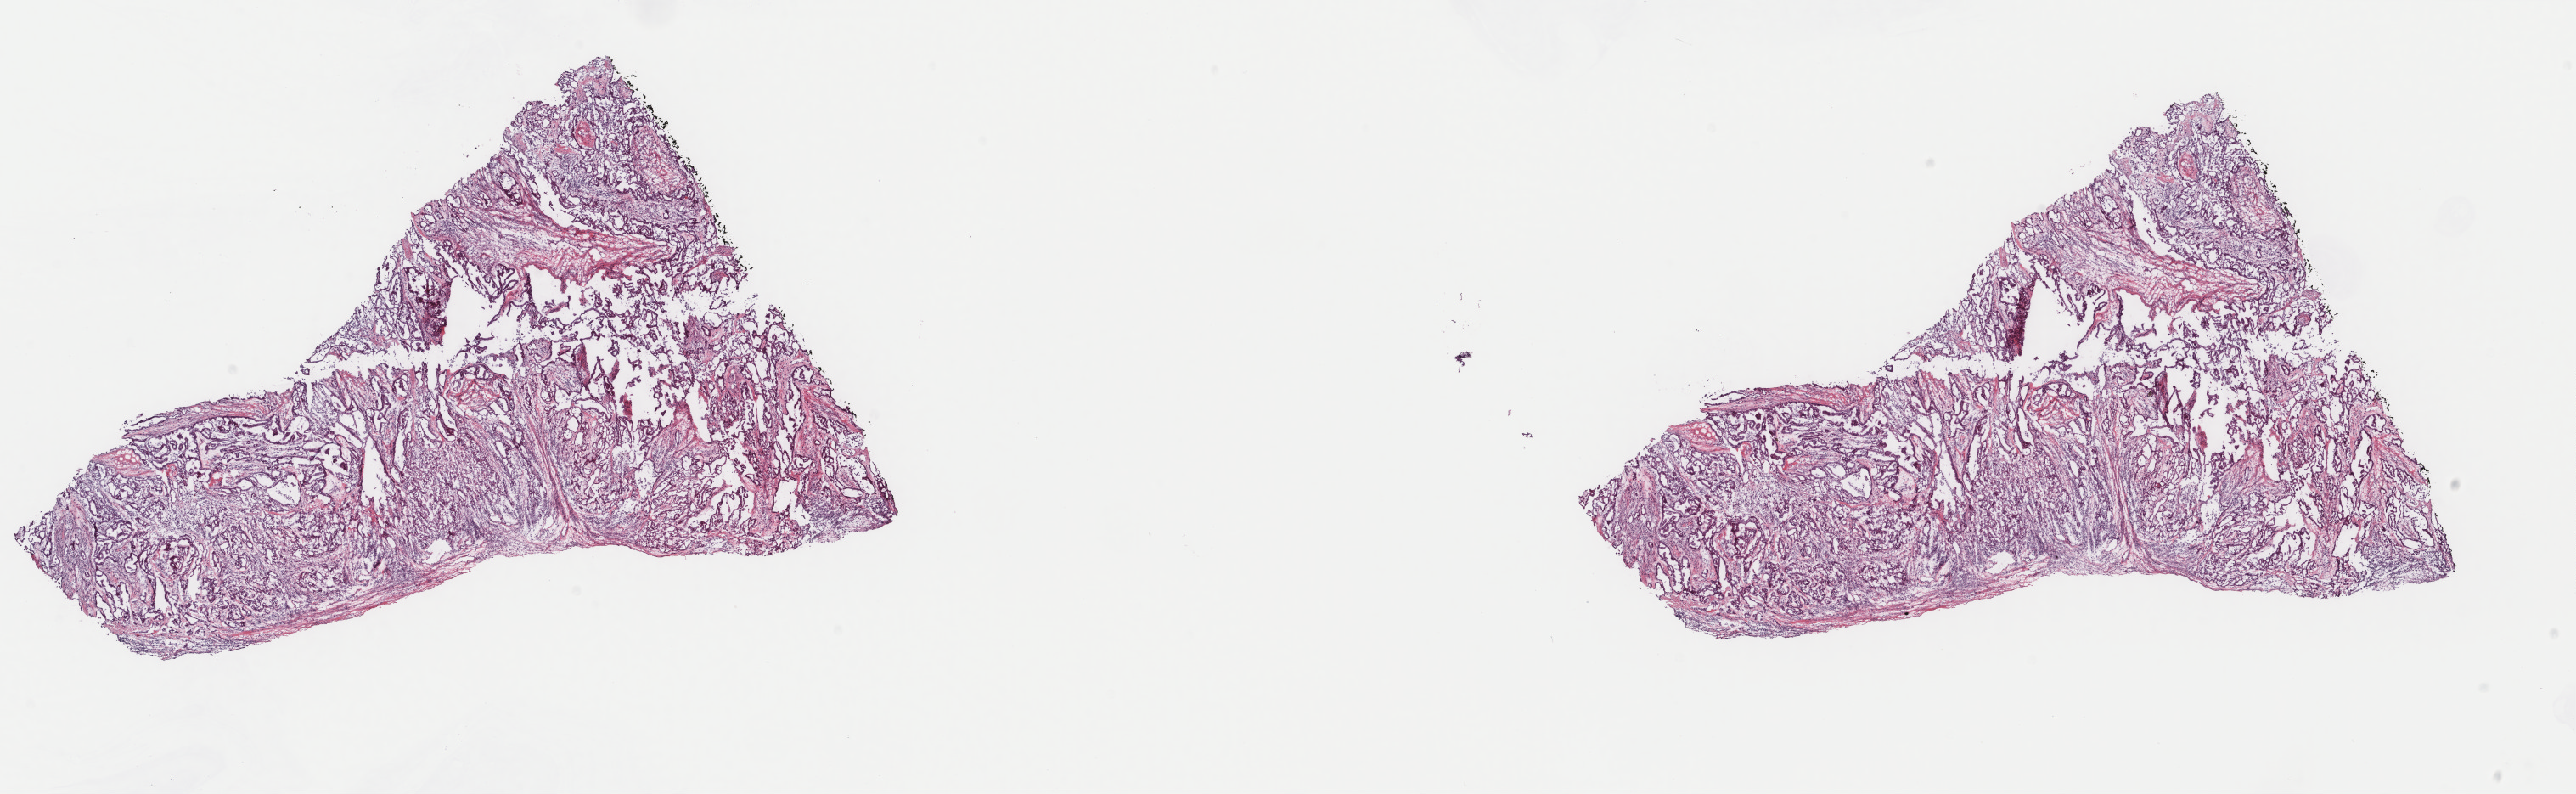
Digitized Hematoxylin and eosin (H&E) stained tissue section (whole slide), shown as a low-resolution overview of the whole scanned area (about 24.1 x 7.4 mm), frozen section from the top of the tissue portion, sample: primary tumour, mesothelium. Patient: male, age at initial diagnosis 66 years. Pathologist review of this section (percent, as recorded): tumour cells 100%, tumour nuclei 65%, normal cells 0%, stromal cells 0%, necrosis 0%. Infiltration values recorded for this section: lymphocyte infiltration 2%, monocyte infiltration 0%, neutrophil infiltration 0%.
Histologic diagnosis: Mesothelioma, malignant (pleura, NOS). AJCC pathologic stage: II (7th edition).